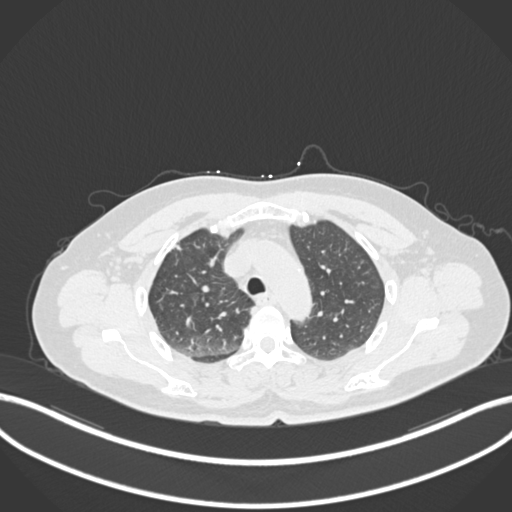
Chest CT, one axial slice. Position 176 of 223 along the scan axis. Reconstruction kernel B30f. 120 kVp. Lung window (W 1500 / L -600 HU). 1 mm slice thickness. 512 × 512 image matrix, field of view 400 × 400 mm. Patient: female, 56 years. From the clinical record (not read from this slice): clinical TNM (as recorded): T1c N0 M0.
Annotated regions visible in this slice (bounding box drawn by a radiologist):
- lung tumour (recorded histology: adenocarcinoma): bounding box <171,240,189,257> (left, top, right, bottom; pixels)